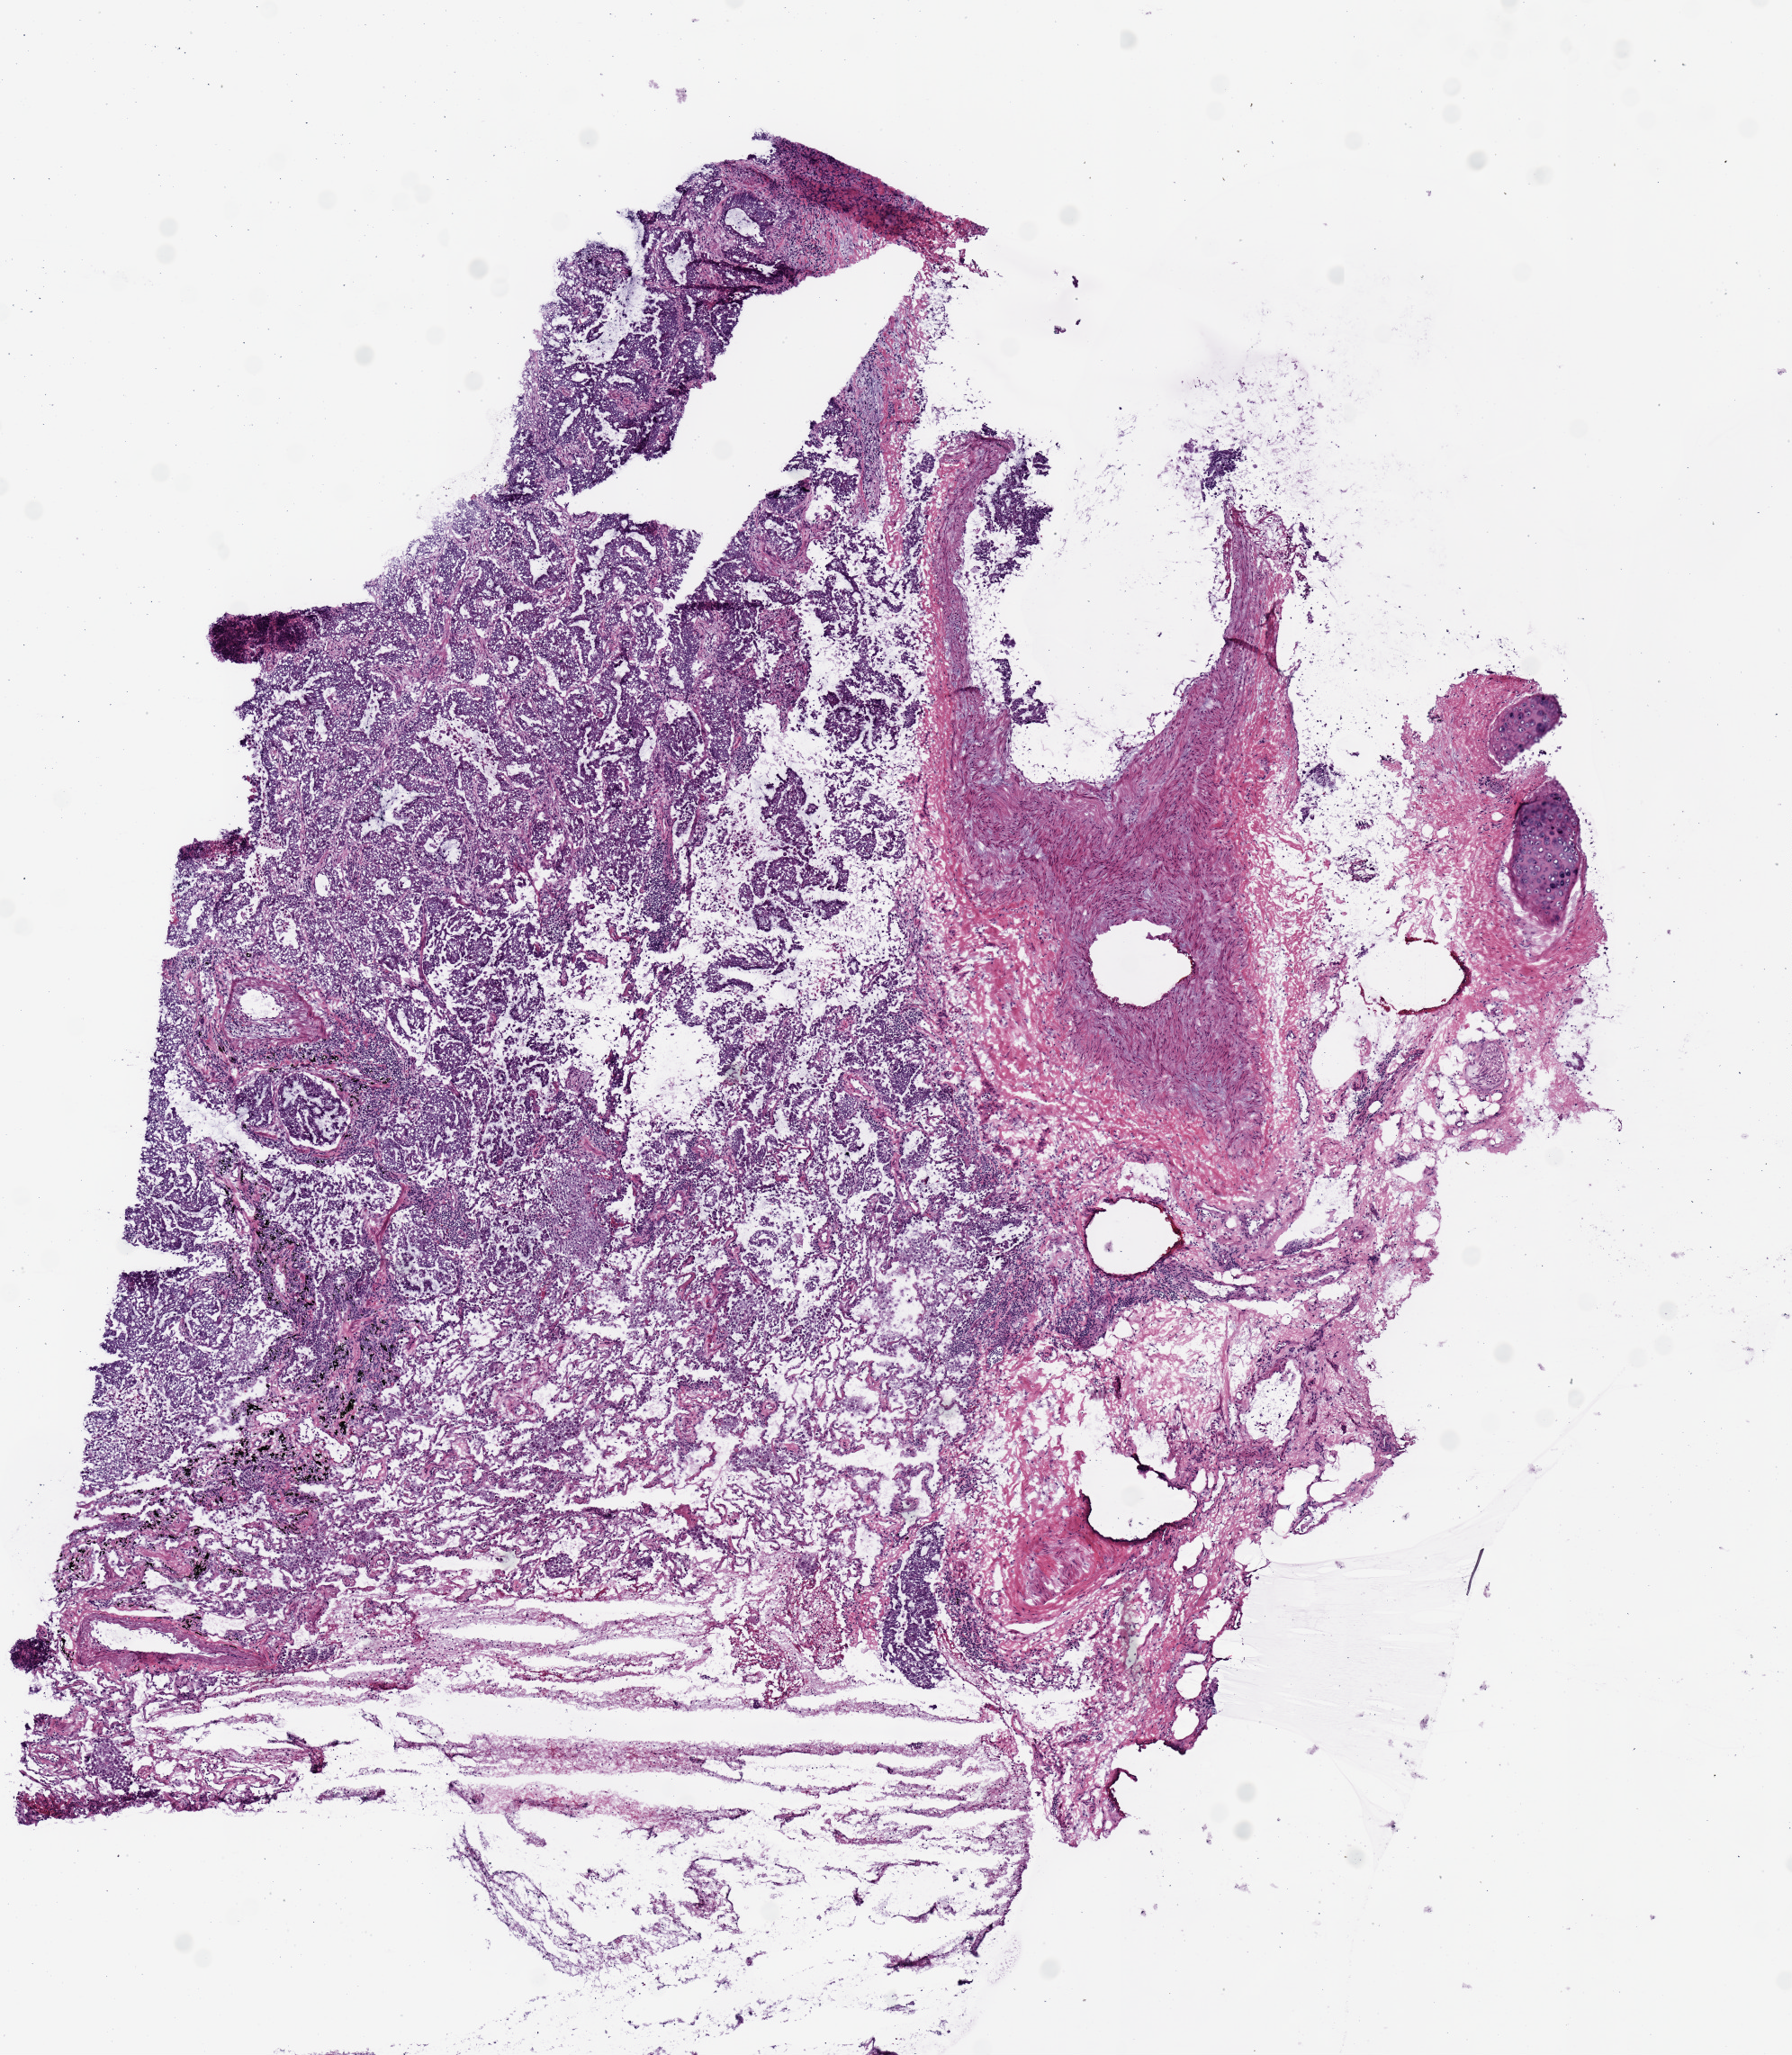
Digitized Hematoxylin and eosin (H&E) stained tissue section (whole slide) — a low-resolution overview of the entire scanned area, about 7.9 x 9.0 mm (slide scanned at 20x); frozen section from the top of the tissue portion; lung, primary tumour sample. Patient: male, age at initial diagnosis 77 years. Composition of this section per pathologist review: tumour nuclei 75%, necrosis 5%.
- AJCC pathologic stage: IB
- diagnosis: Adenocarcinoma, NOS (lower lobe, lung)
- TNM: T2a N0 MX